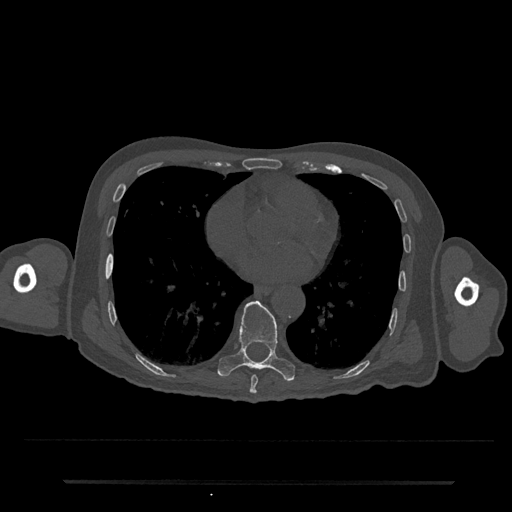
CT including the spine, one axial slice. Position 376 of 797 along the scan axis. Reconstruction kernel Br40s/3. 120 kVp. Bone window (W 1800 / L 400 HU). 512 × 512 image matrix. Patient: male, 74 years. Case-level facts recorded for this patient, not image findings: primary cancer: prostate.
Structures marked on this image (semi-automatically segmented with operator editing):
- T8 vertebra: box from (x=250, y=375) to (x=258, y=394) px
- T9 vertebra: (x=218, y=301)–(x=295, y=381)